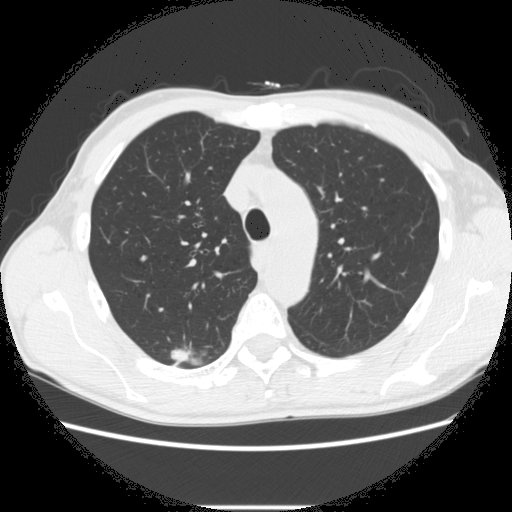
Low-dose screening chest CT, one axial slice. Position 208 of 282 along the scan axis. Lung window (W 1500 / L -600 HU). 2.5 mm slice thickness. 512 × 512 image matrix, field of view 360 × 360 mm.
Annotated regions visible in this slice (outlined manually by an expert reader):
- lesion 1 (tumor, upper lobe of right lung): bounding box [x1, y1, x2, y2] px = [171, 348, 189, 363]